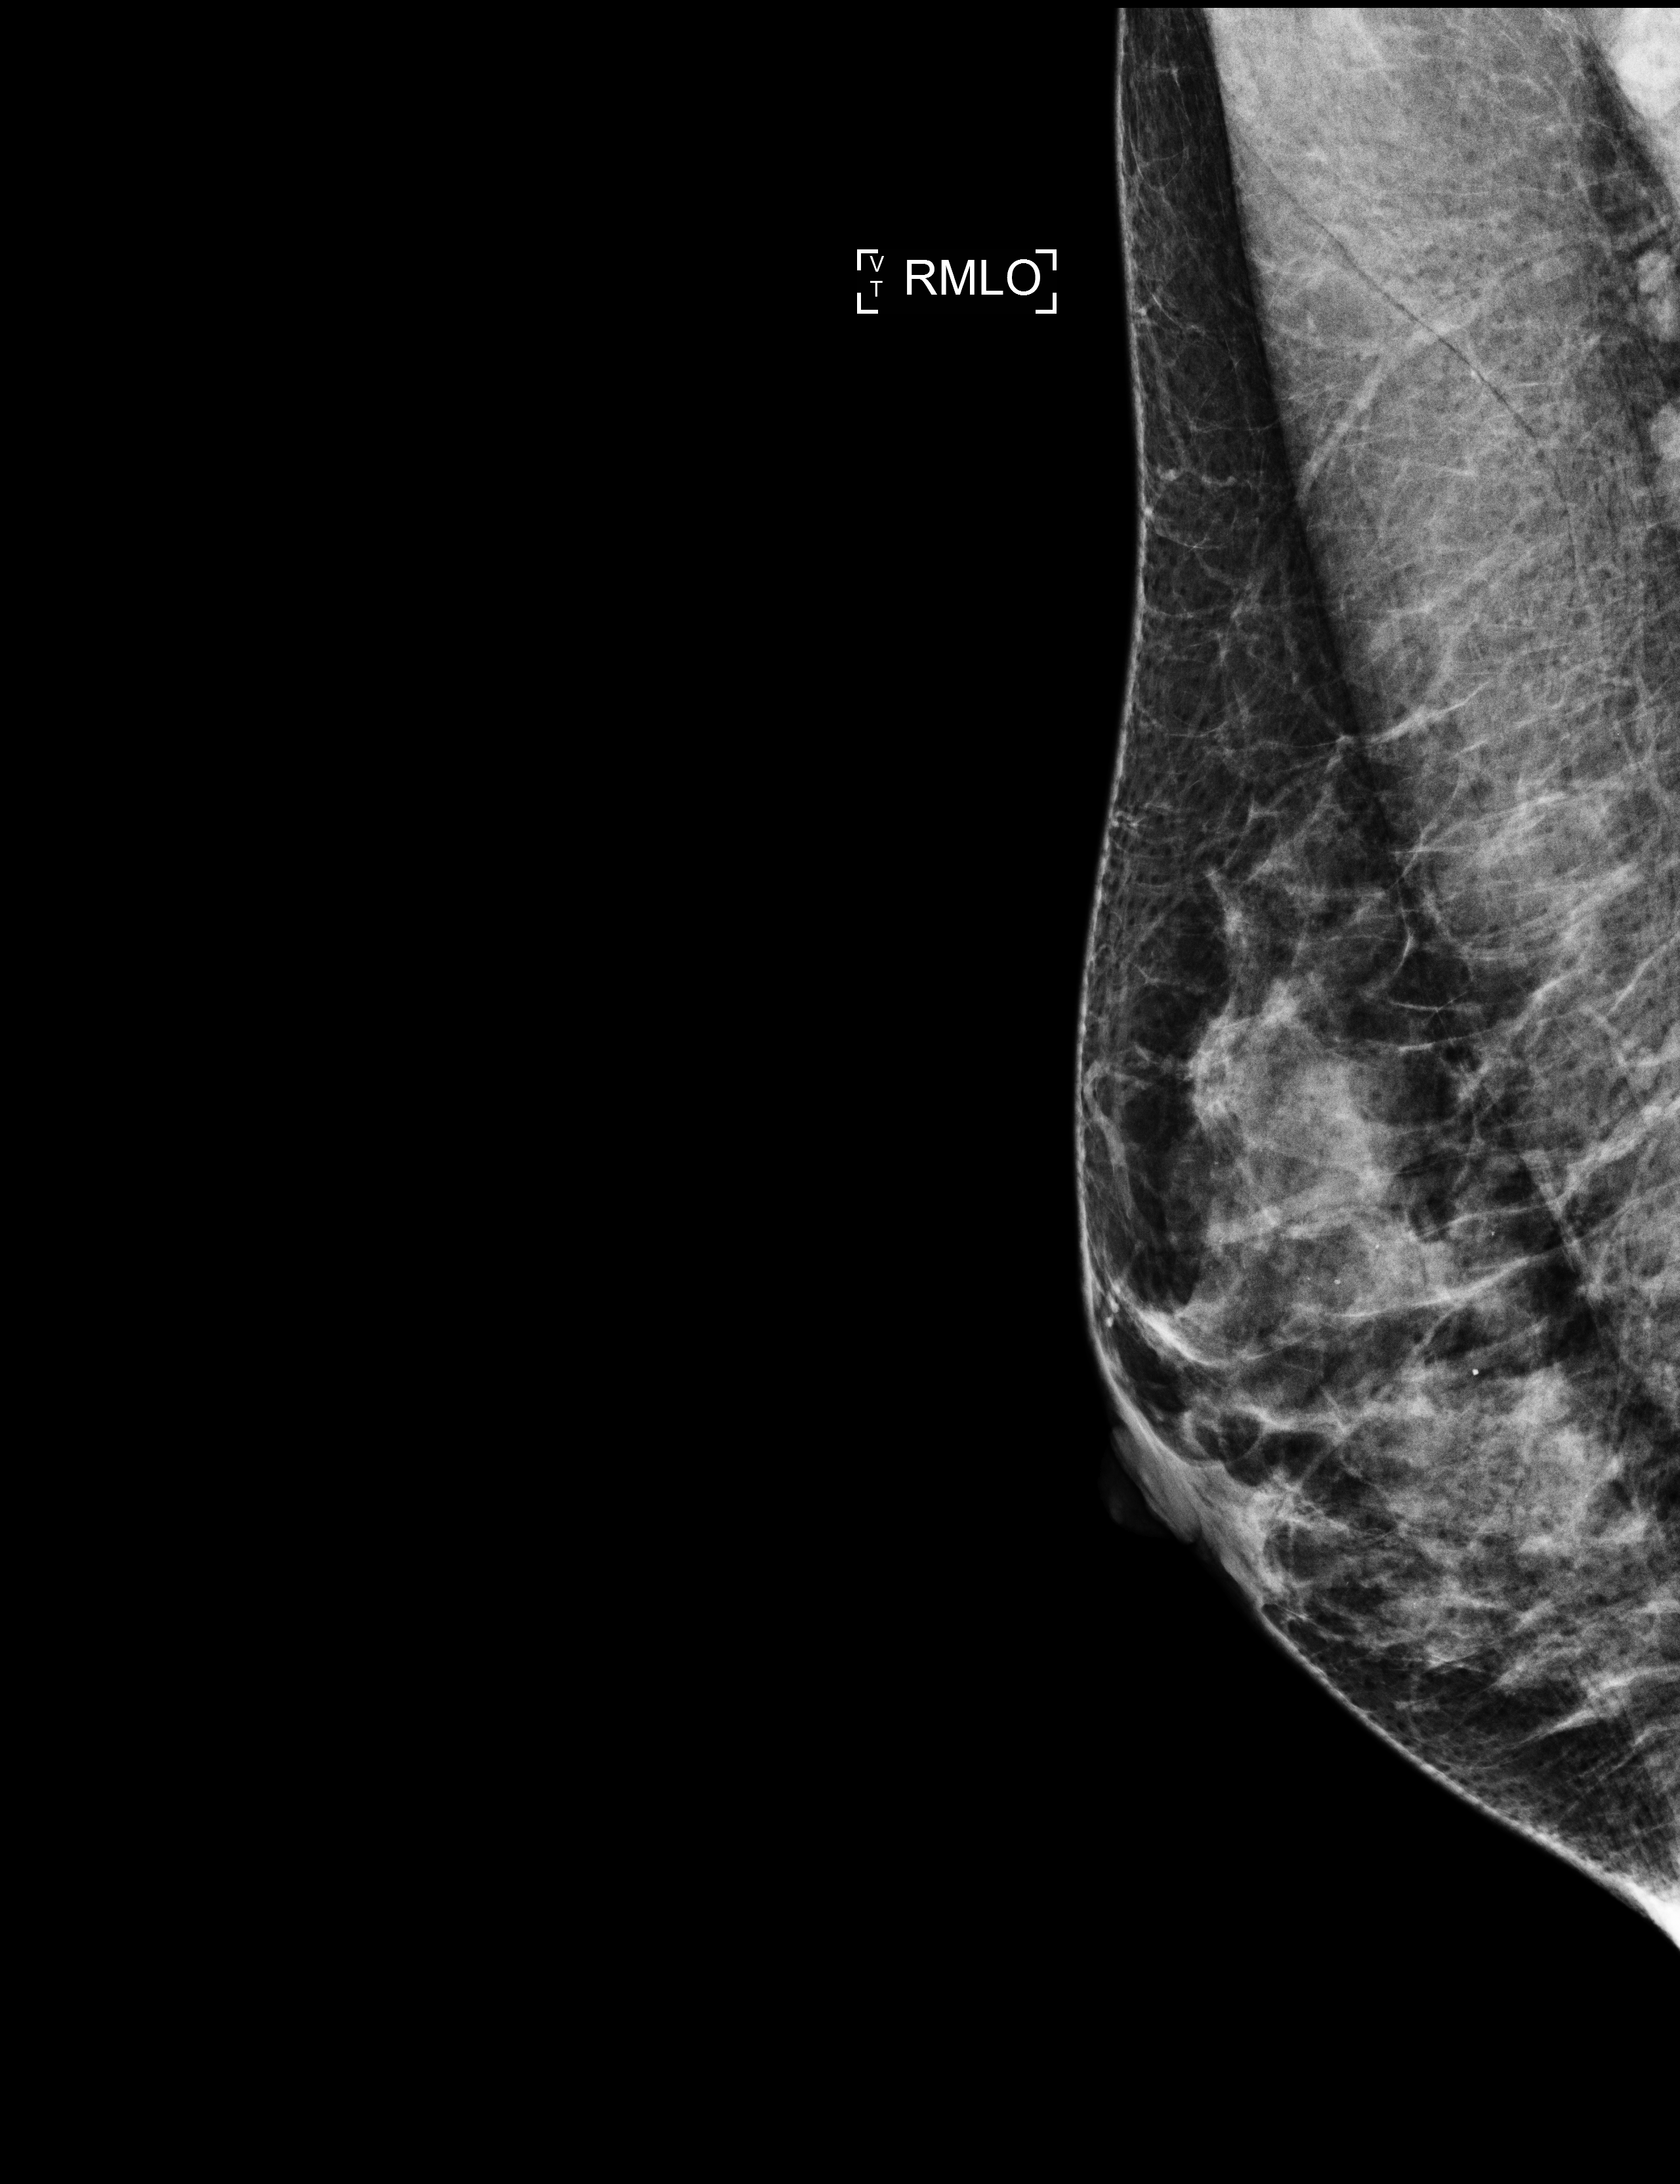
Annual screening mammography examination, compressed breast thickness 42 mm, system: Selenia Dimensions. Patient: female, 48 years.
Image type: full-field digital mammogram. Breast: right. Projection: MLO view.